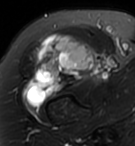
MRI of an extremity soft-tissue mass, one axial slice; slice 74 of 95 in the series (ordered by position); T2-weighted fat-saturated; MR volume resampled by the dataset authors to the PET/CT grid (not the native acquisition matrix); 135 × 146 image matrix. Female patient. From the clinical record (not read from this slice): histological type: pleiomorphic undifferentiated sarcoma; grade: high; site of the primary tumour: right quadricep.
Annotated regions visible in this slice (expert contour drawn on MRI and transferred to this co-registered scan by the dataset authors):
- gross tumour volume including surrounding oedema: bounding box (x1, y1, x2, y2) in pixels: (23, 32, 97, 108)
- gross tumour volume (mass): (23, 32, 97, 108)